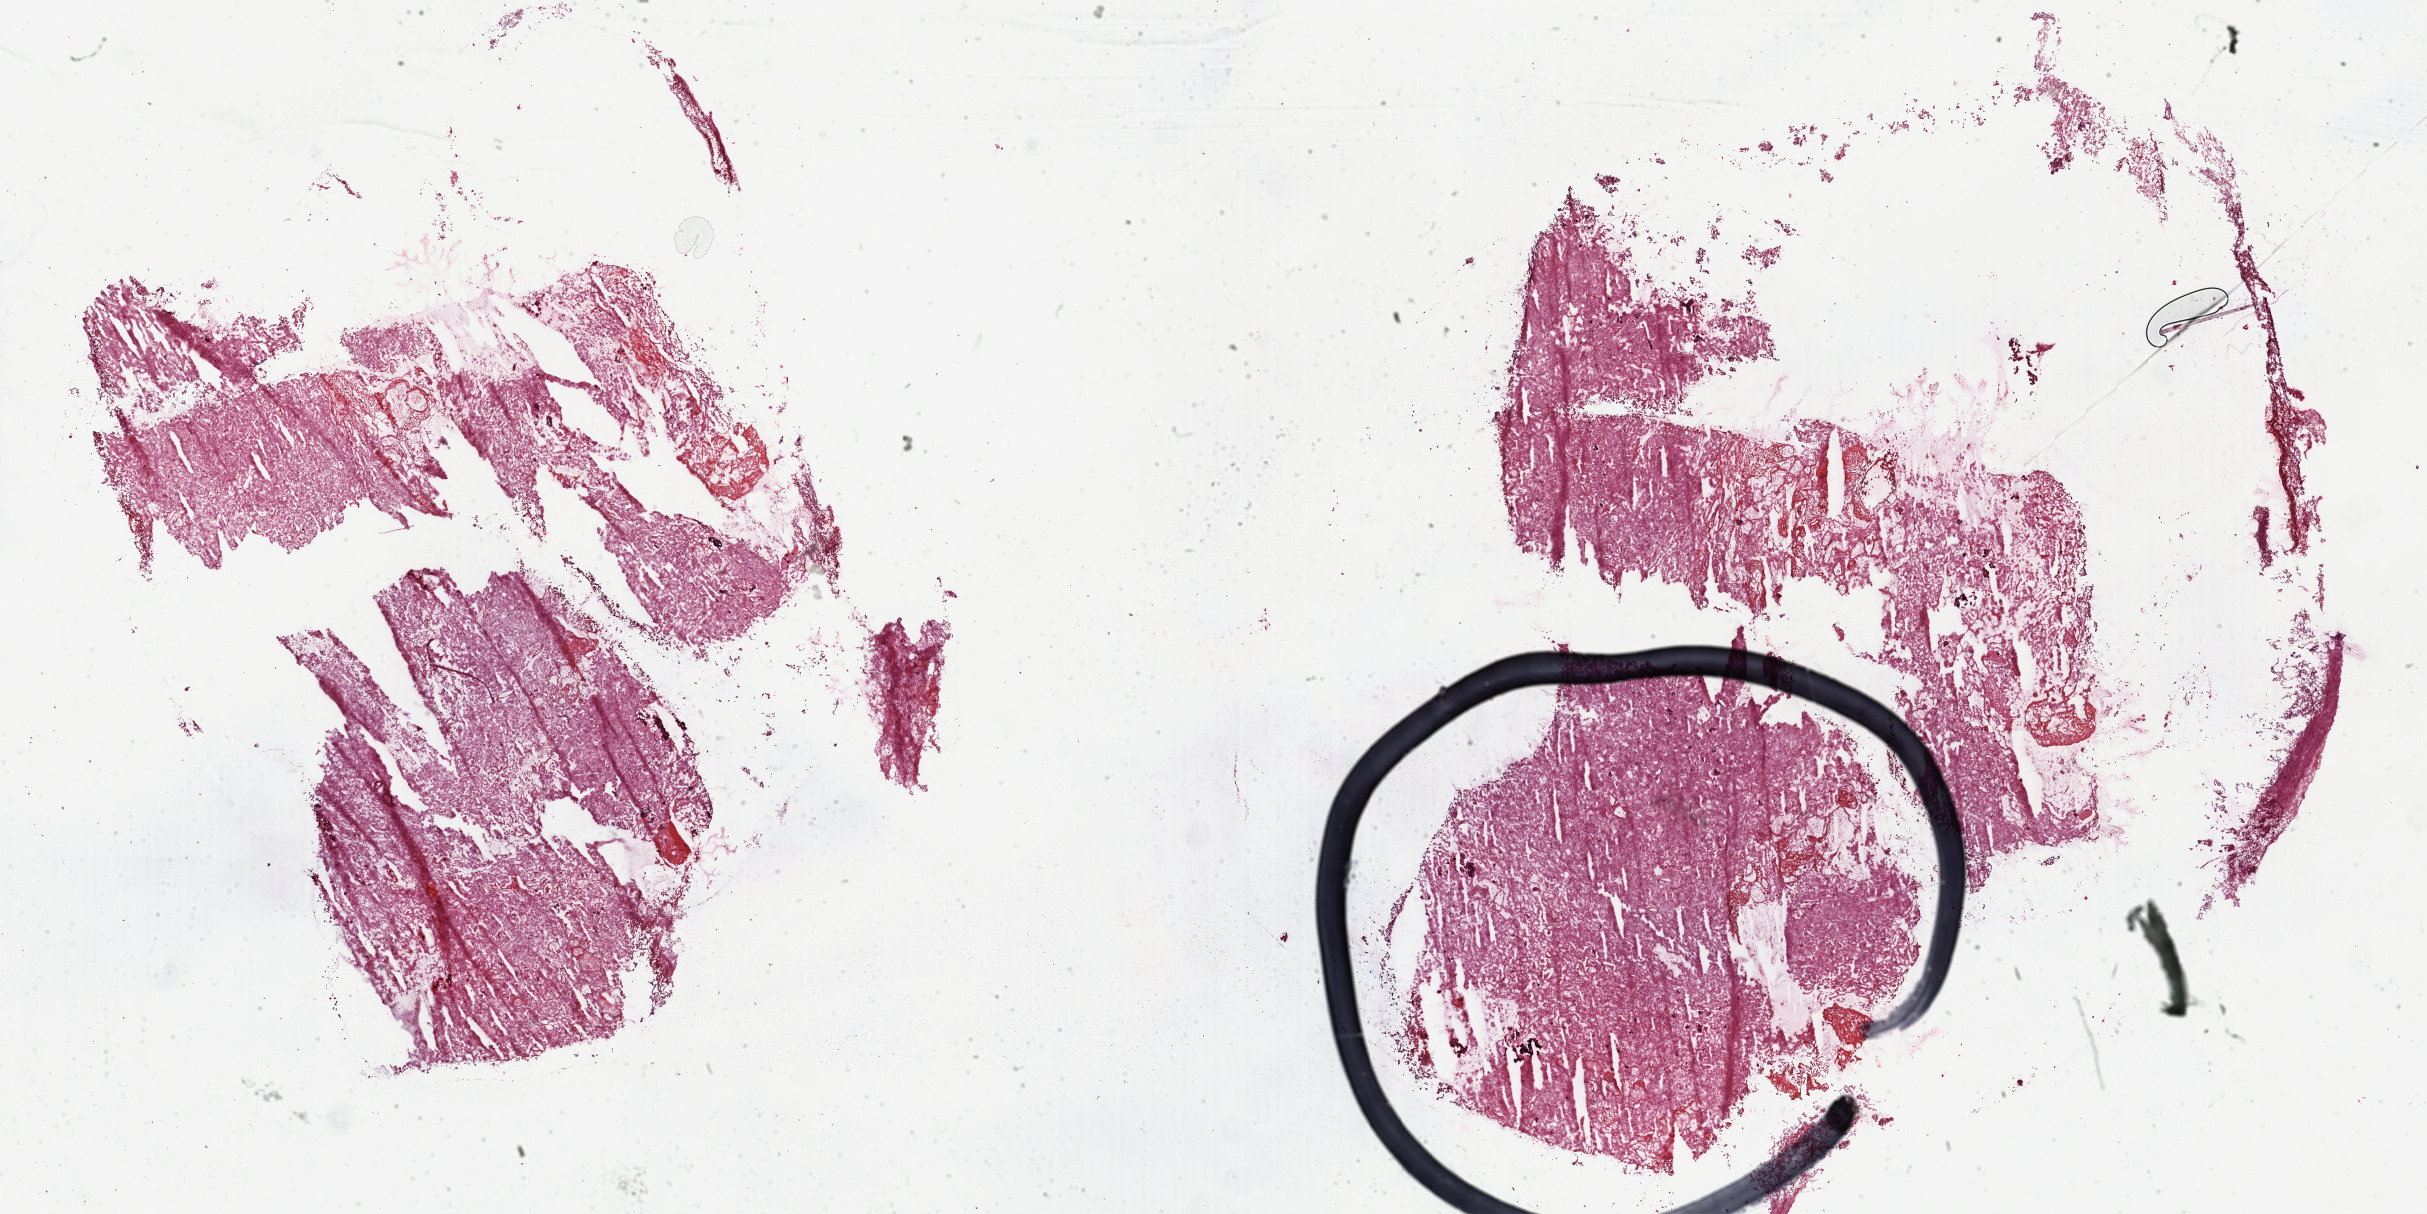
Digitized H&E-stained tissue section (whole slide), a low-resolution overview of the entire scanned area, about 39.3 x 19.6 mm (from a 40x scan), frozen section from the top of the tissue portion, primary tumour sample from the kidney. Patient: male, age at initial diagnosis 77 years. Pathologist review of this section (percent, as recorded): tumour cells 100%, tumour nuclei 75%, normal cells 0%, stromal cells 0%, necrosis 0%. Infiltration values recorded for this section: lymphocyte infiltration 1%, monocyte infiltration 8%, neutrophil infiltration 0%.
Pathologic diagnosis: Papillary adenocarcinoma, NOS.